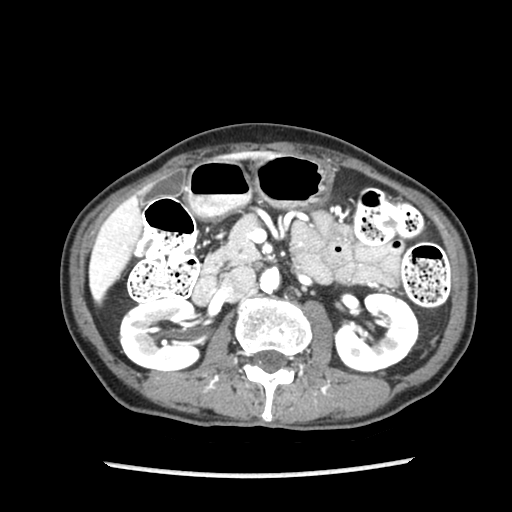
Contrast-enhanced abdominal CT (liver protocol), one axial slice; position 39 of 87 along the scan axis; reconstruction kernel STANDARD; 140 kVp; soft-tissue window (W 400 / L 40 HU); 2.5 mm slice thickness; 512 × 512 image matrix, field of view 300 × 300 mm. Case-level facts recorded for this patient, not image findings: diagnosis: hepatocellular carcinoma (patient treated with transarterial chemoembolisation; whether this scan precedes or follows treatment is not stated here); TNM stage (as recorded): Stage-IIIB; Child-Pugh class: A; tumour differentiation: well differentiated; tumour nodularity: uninodular.
Structures marked on this image (semi-automatically segmented with operator editing):
- liver parenchyma outside the tumour (the mass and vessels are separate outlines, so this box may not span the whole liver): bounding box (x1, y1, x2, y2) in pixels: (90, 196, 140, 302)
- liver vessels: (92, 220, 131, 288)